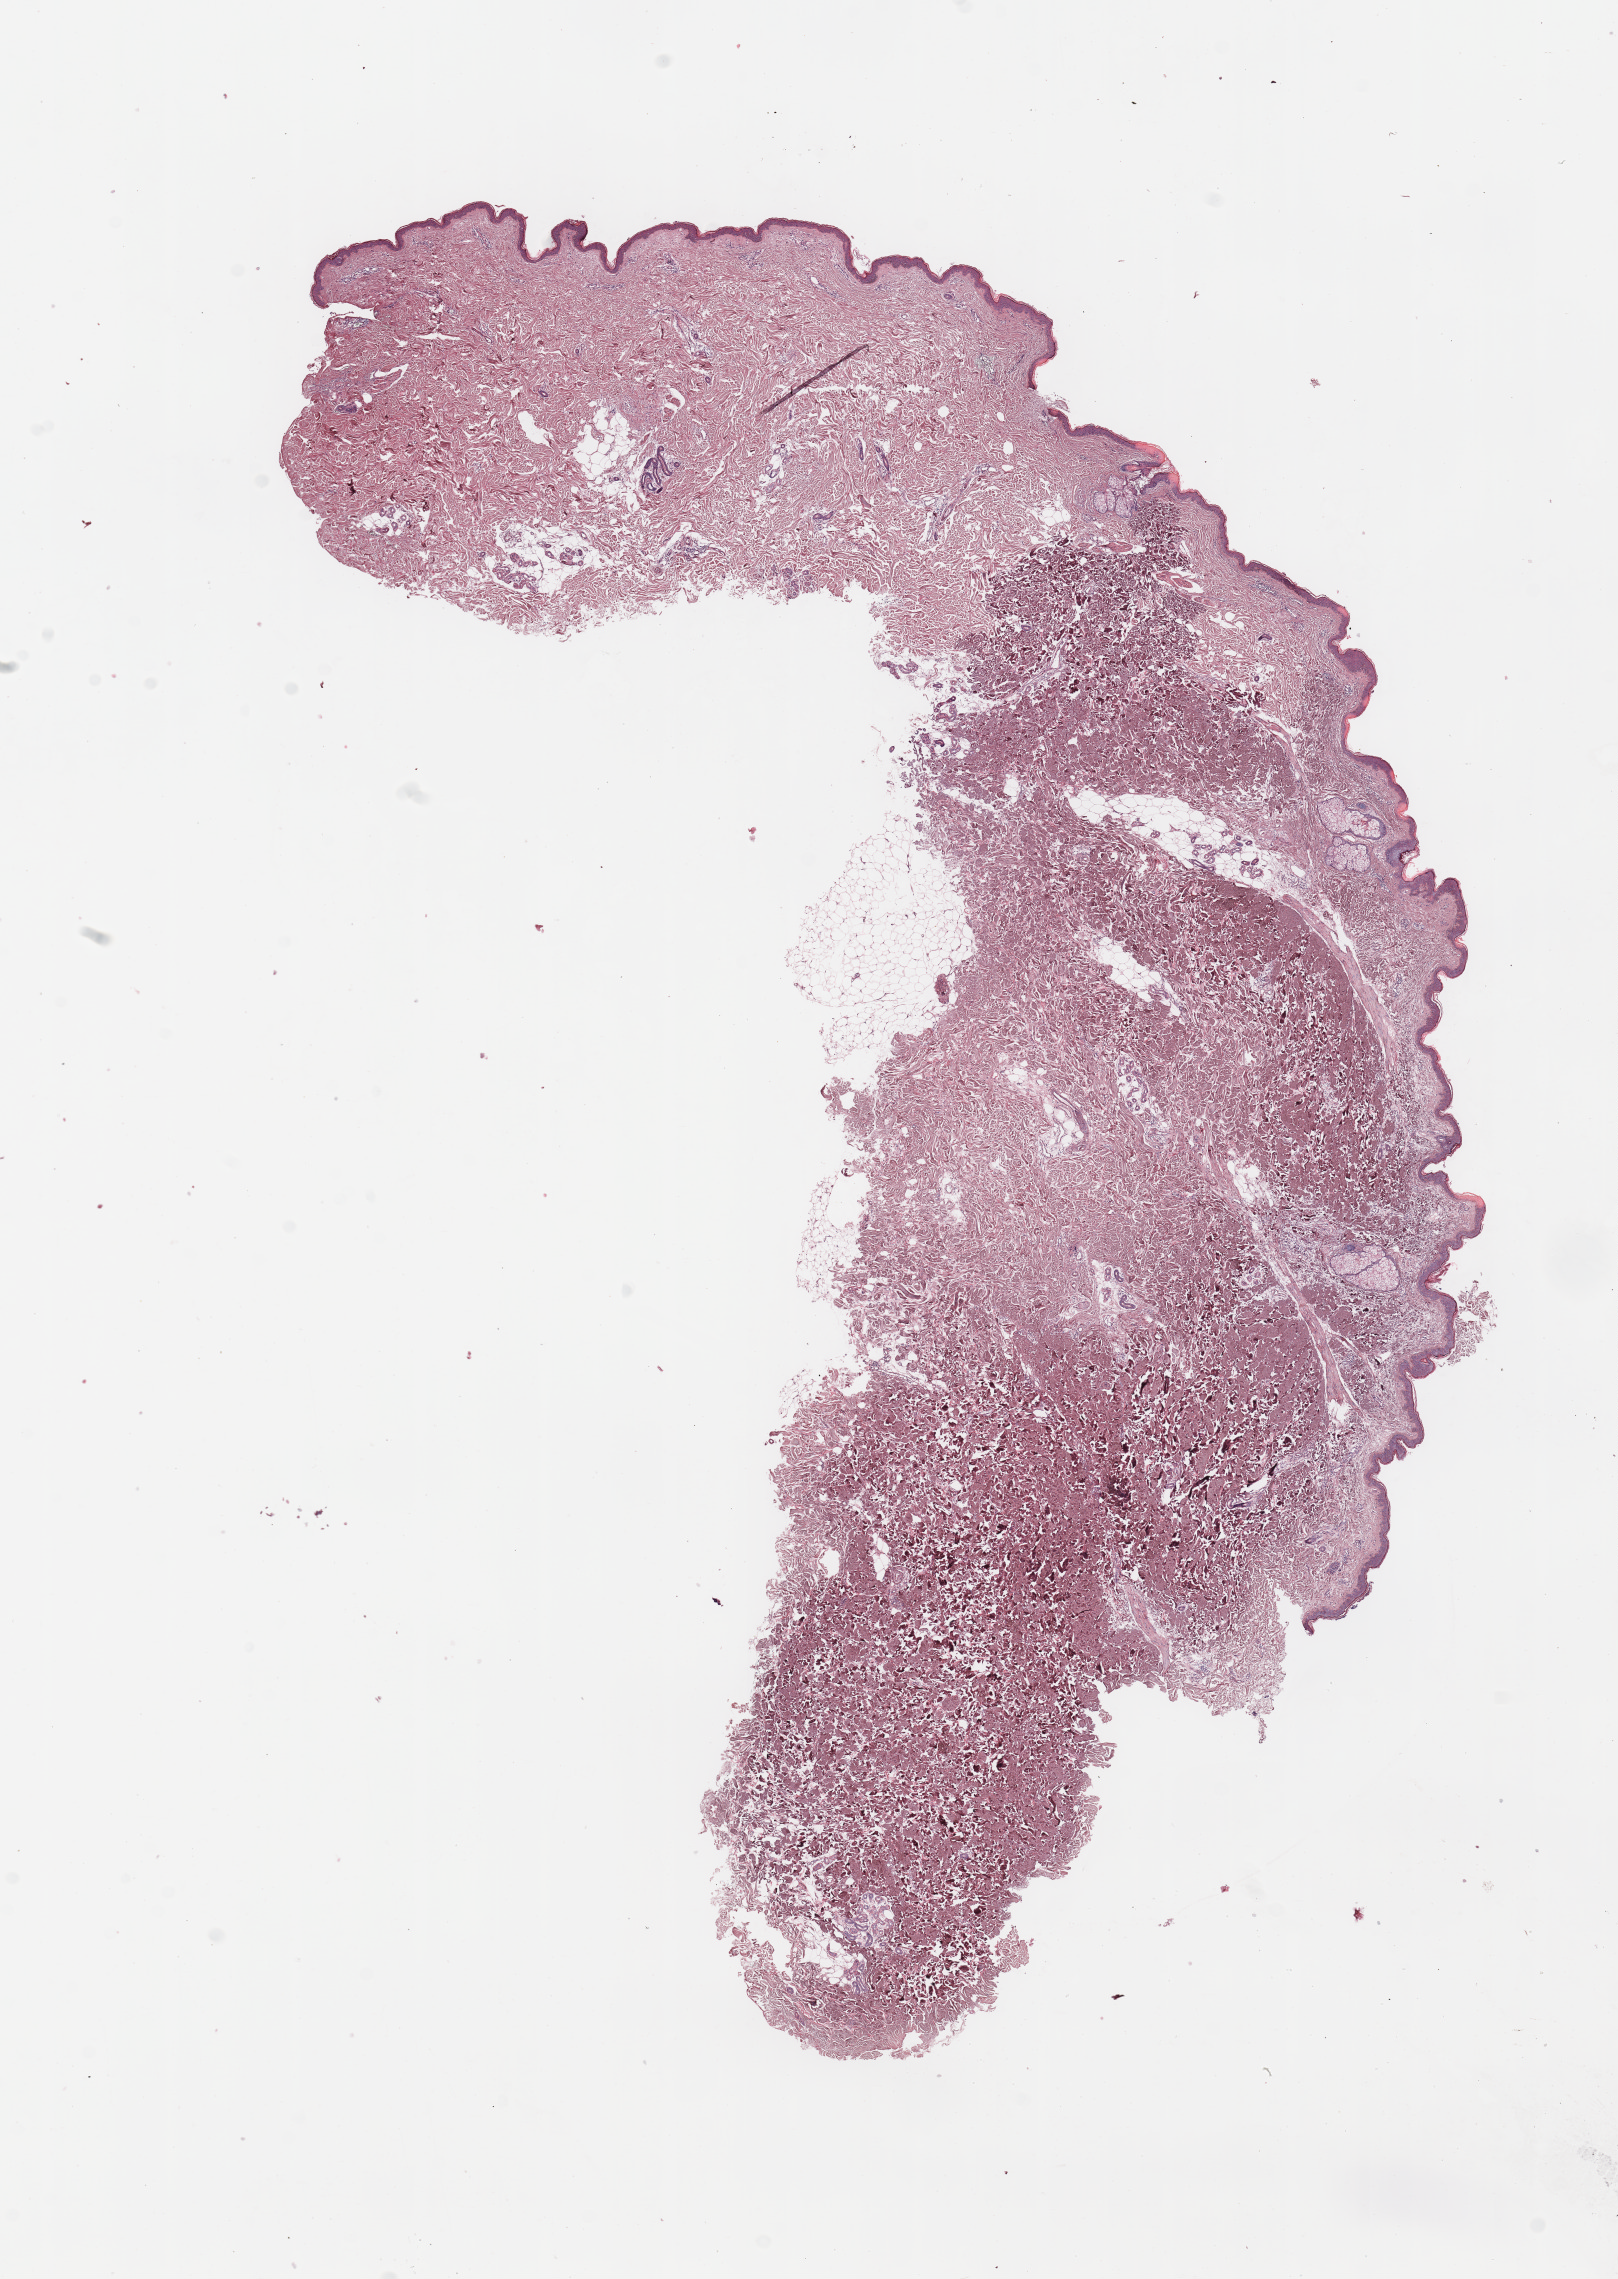
H&E whole-slide image — low-resolution overview of the scanned area, about 12.8 x 18.0 mm, normal (non-tumour) tissue sample, sampled site: trunk. 80-year-old female patient.
This section: normal (non-tumour) tissue from the same patient. Patient diagnosis: Malignant melanoma, NOS.